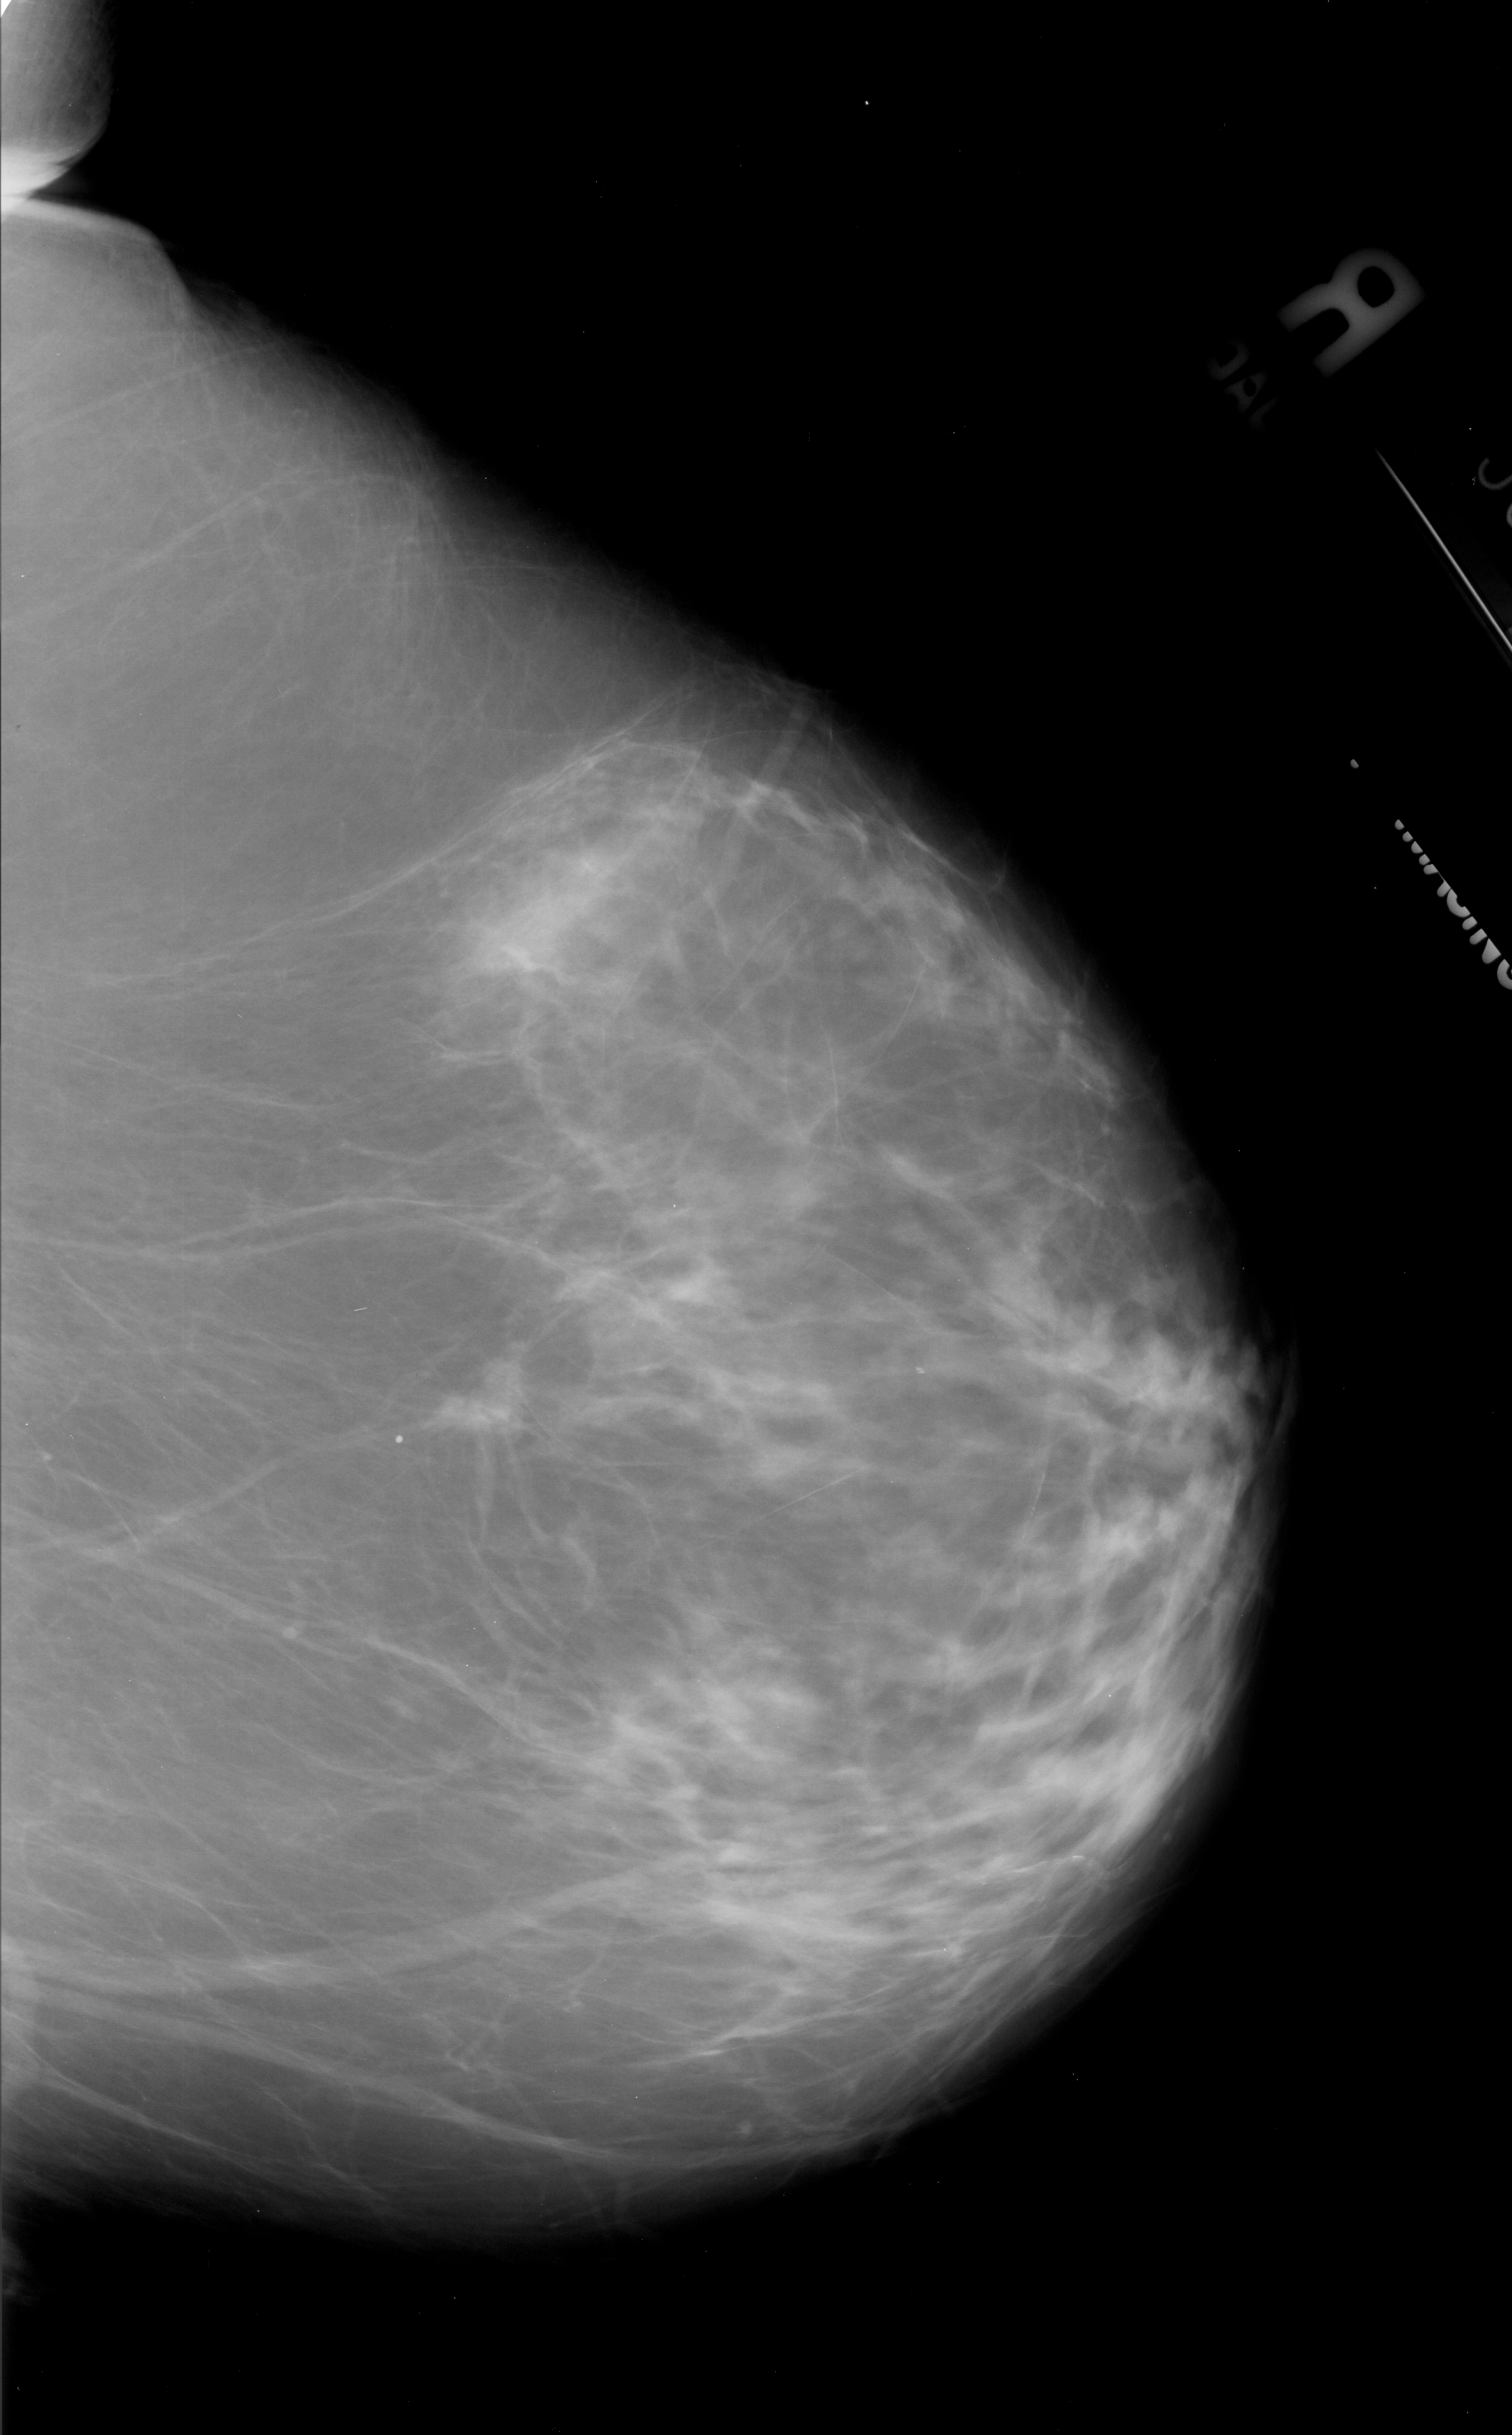
Digitized screen-film mammogram, right breast, craniocaudal (CC) view, BI-RADS breast density category 2 (scale 1–4).
Mass, shape irregular, margins spiculated; BI-RADS assessment category 5; subtlety rating 2 on a 1 (subtle) to 5 (obvious) scale; pathology (as recorded): malignant.